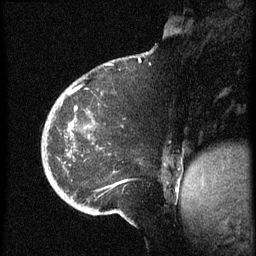
Breast MRI (dynamic contrast-enhanced), one sagittal slice; position 17 of 60 along the scan axis; dynamic contrast-enhanced series, image 2 of 3 at this slice position (ordered by acquisition); 1.5 T; TE 4.2 ms, TR 8.4 ms; 2.5 mm slice thickness; 256 × 256 image matrix, field of view 200 × 200 mm. Female patient, age 38 years. From the clinical record (not read from this slice): setting: breast cancer imaged before/during neoadjuvant chemotherapy; receptor status: HER2-positive.
Structures marked on this image (semi-automatically segmented with operator editing):
- analysis volume of interest (the breast-tissue region the enhancement analysis was run in; not a lesion): bounding box <42,75,173,202> (left, top, right, bottom; pixels)
- tumour enhancement mask (voxels above the 70 % enhancement threshold inside the analysis volume of interest): <70,93,72,95>